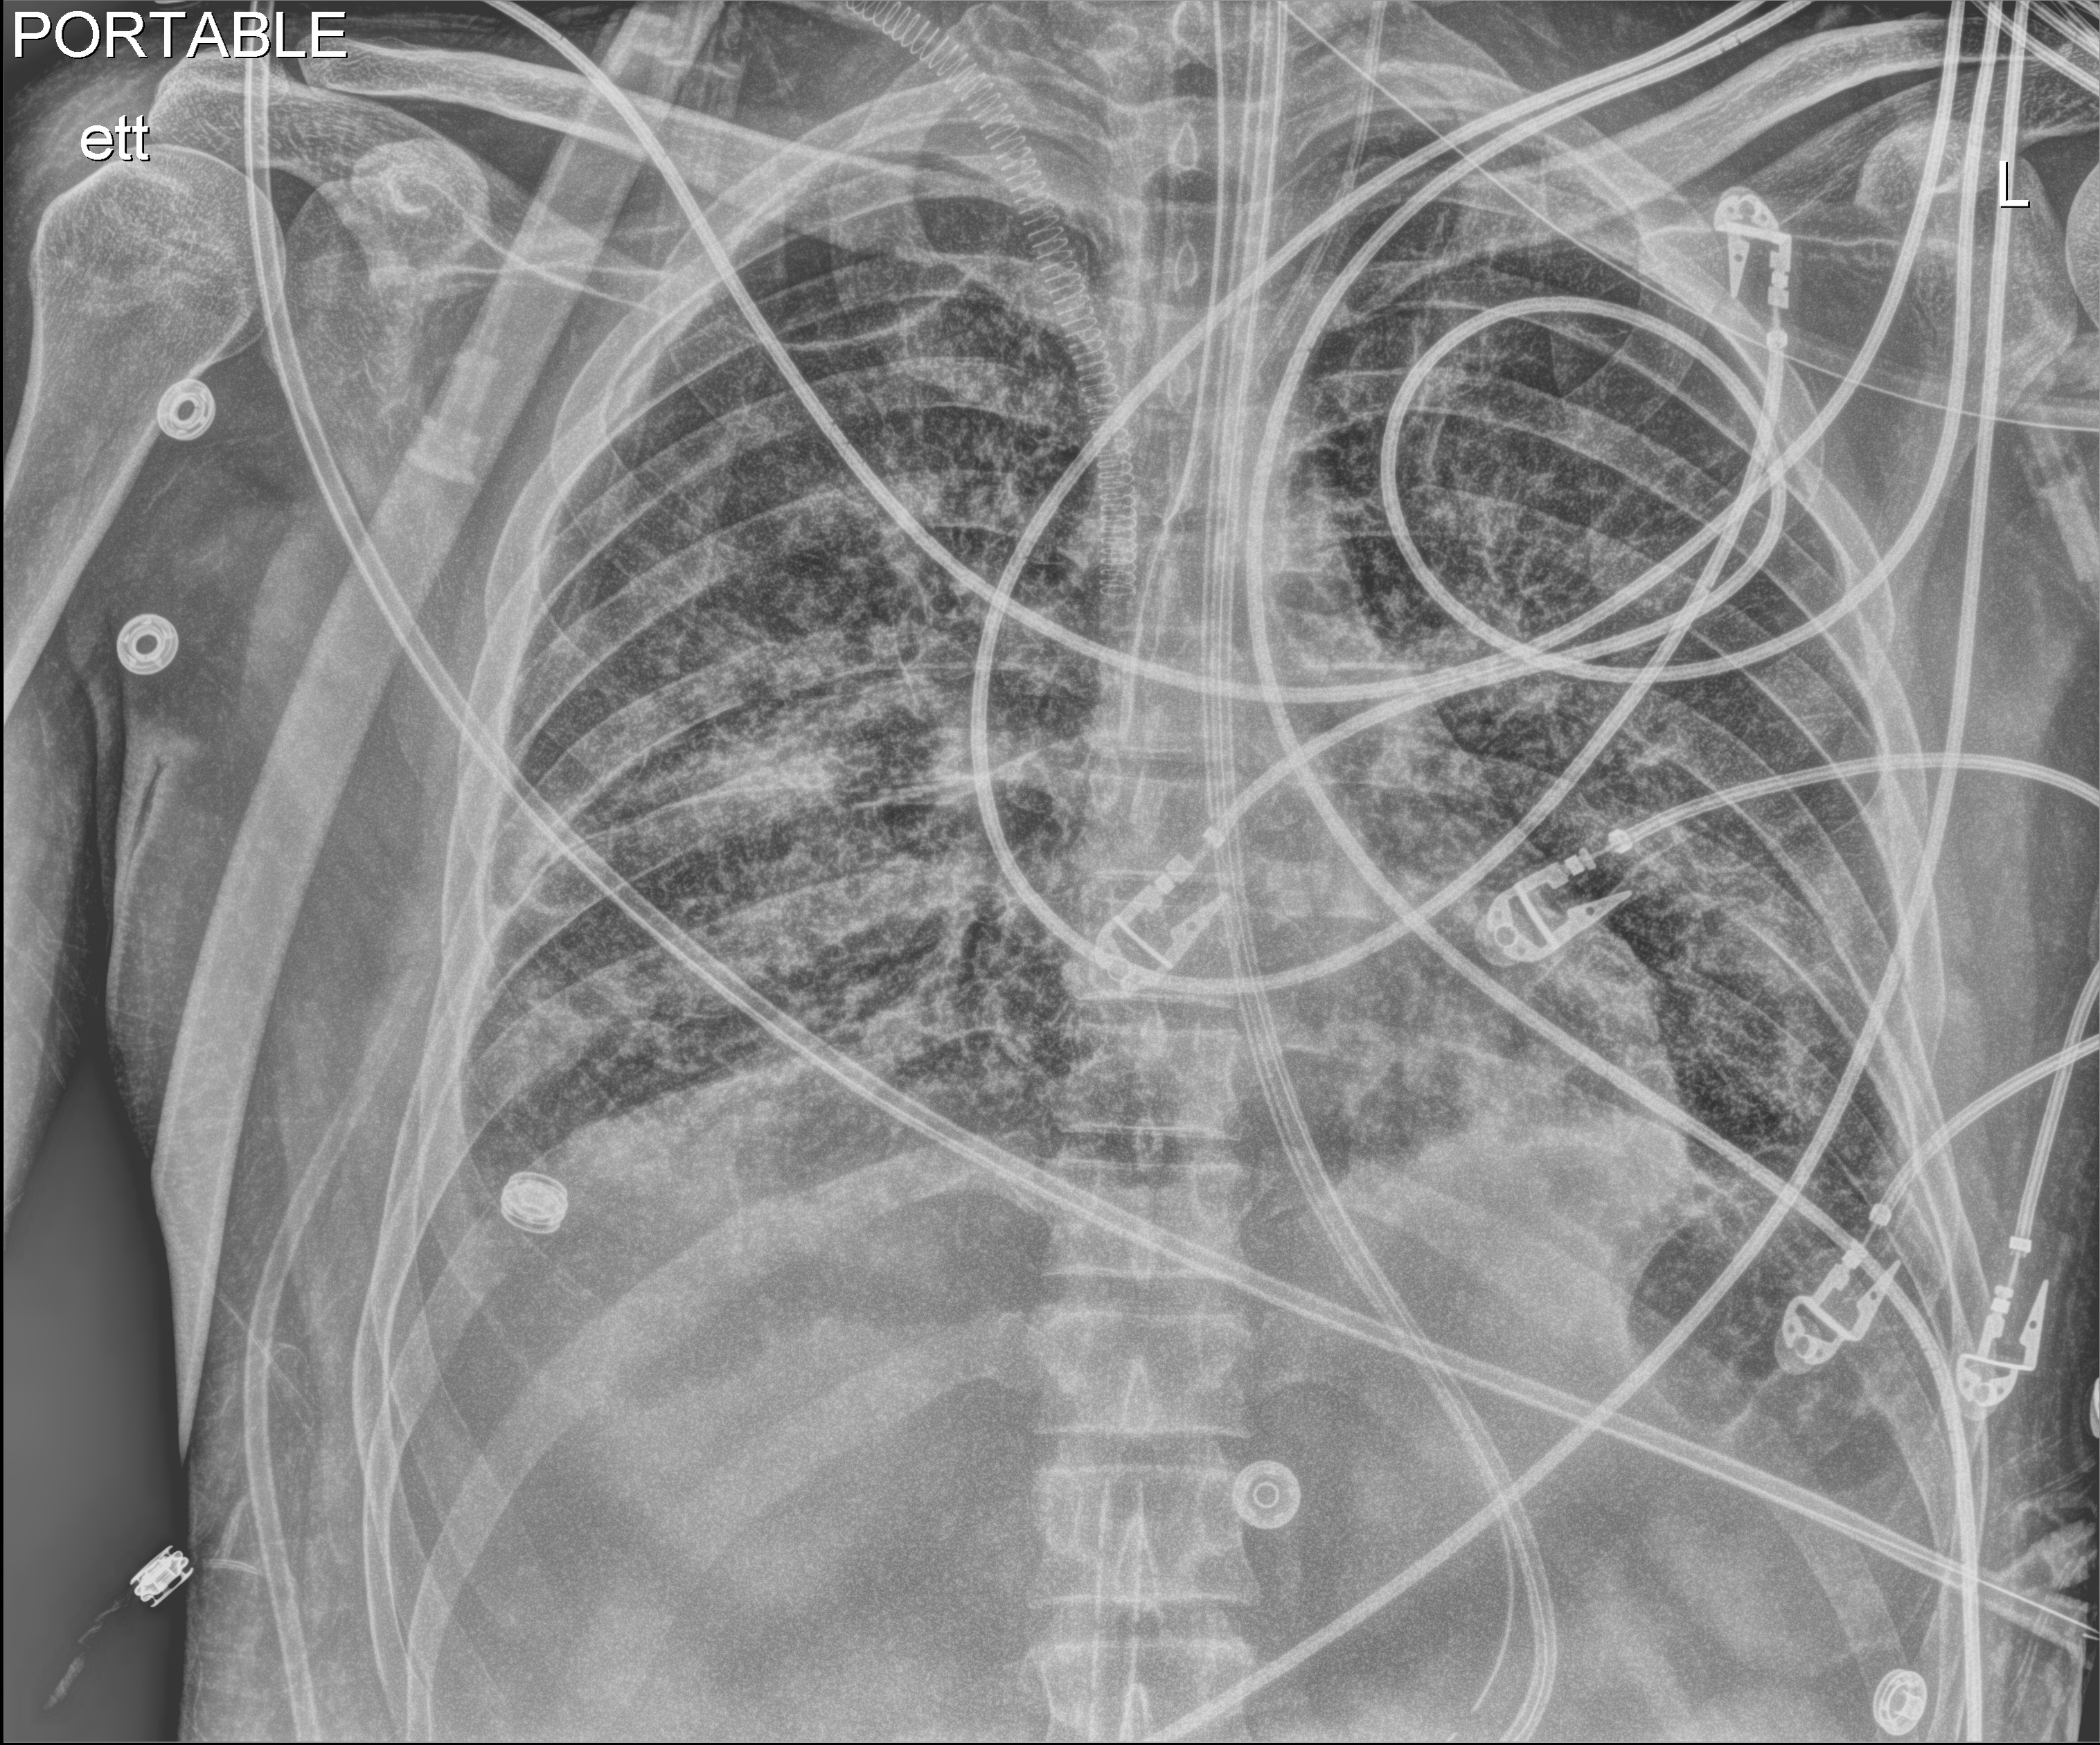
Portable chest radiograph, anteroposterior (AP) projection. Adult patient hospitalised with COVID-19, age 18–59 years.
Hospital-stay facts (about this admission, not read from this image; timing relative to this image not recorded): smoking status (admission record): never; admitted to intensive care during this hospital stay: yes; mechanically ventilated during this hospital stay: yes.